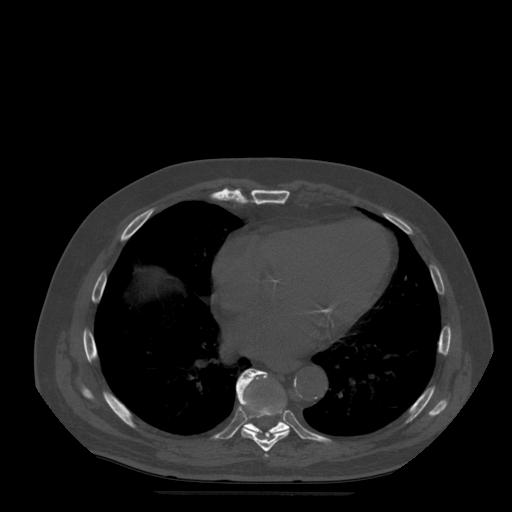
CT including the spine, one axial slice; position 304 of 522 along the scan axis; bone window (W 1800 / L 400 HU); 1.25 mm slice thickness; 512 × 512 image matrix. Patient age 72 years. Case-level facts recorded for this patient, not image findings: primary cancer: prostate.
Annotated regions visible in this slice (semi-automatically segmented with operator editing):
- T7 vertebra: box from (x=265, y=454) to (x=268, y=457) px
- T8 vertebra: (x=236, y=371)–(x=290, y=452)
- T9 vertebra: (x=239, y=369)–(x=289, y=436)